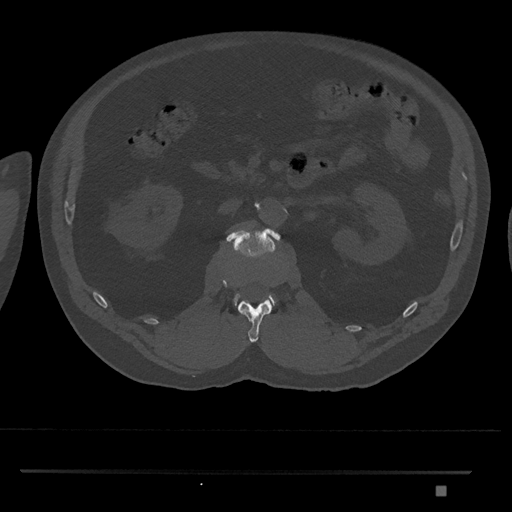
CT including the spine, one axial slice. Position 794 of 1134 along the scan axis. Reconstruction kernel Br40s/3. 120 kVp. Bone window (W 1800 / L 400 HU). 0.5 mm slice thickness. 512 × 512 image matrix, field of view 429 × 429 mm. Patient: male, 65 years. Case-level facts recorded for this patient, not image findings: primary cancer: prostate.
Structures marked on this image (semi-automatically segmented with operator editing):
- L1 vertebra: bounding box (x1, y1, x2, y2) in pixels: (238, 299, 272, 343)
- L2 vertebra: (226, 228, 281, 307)